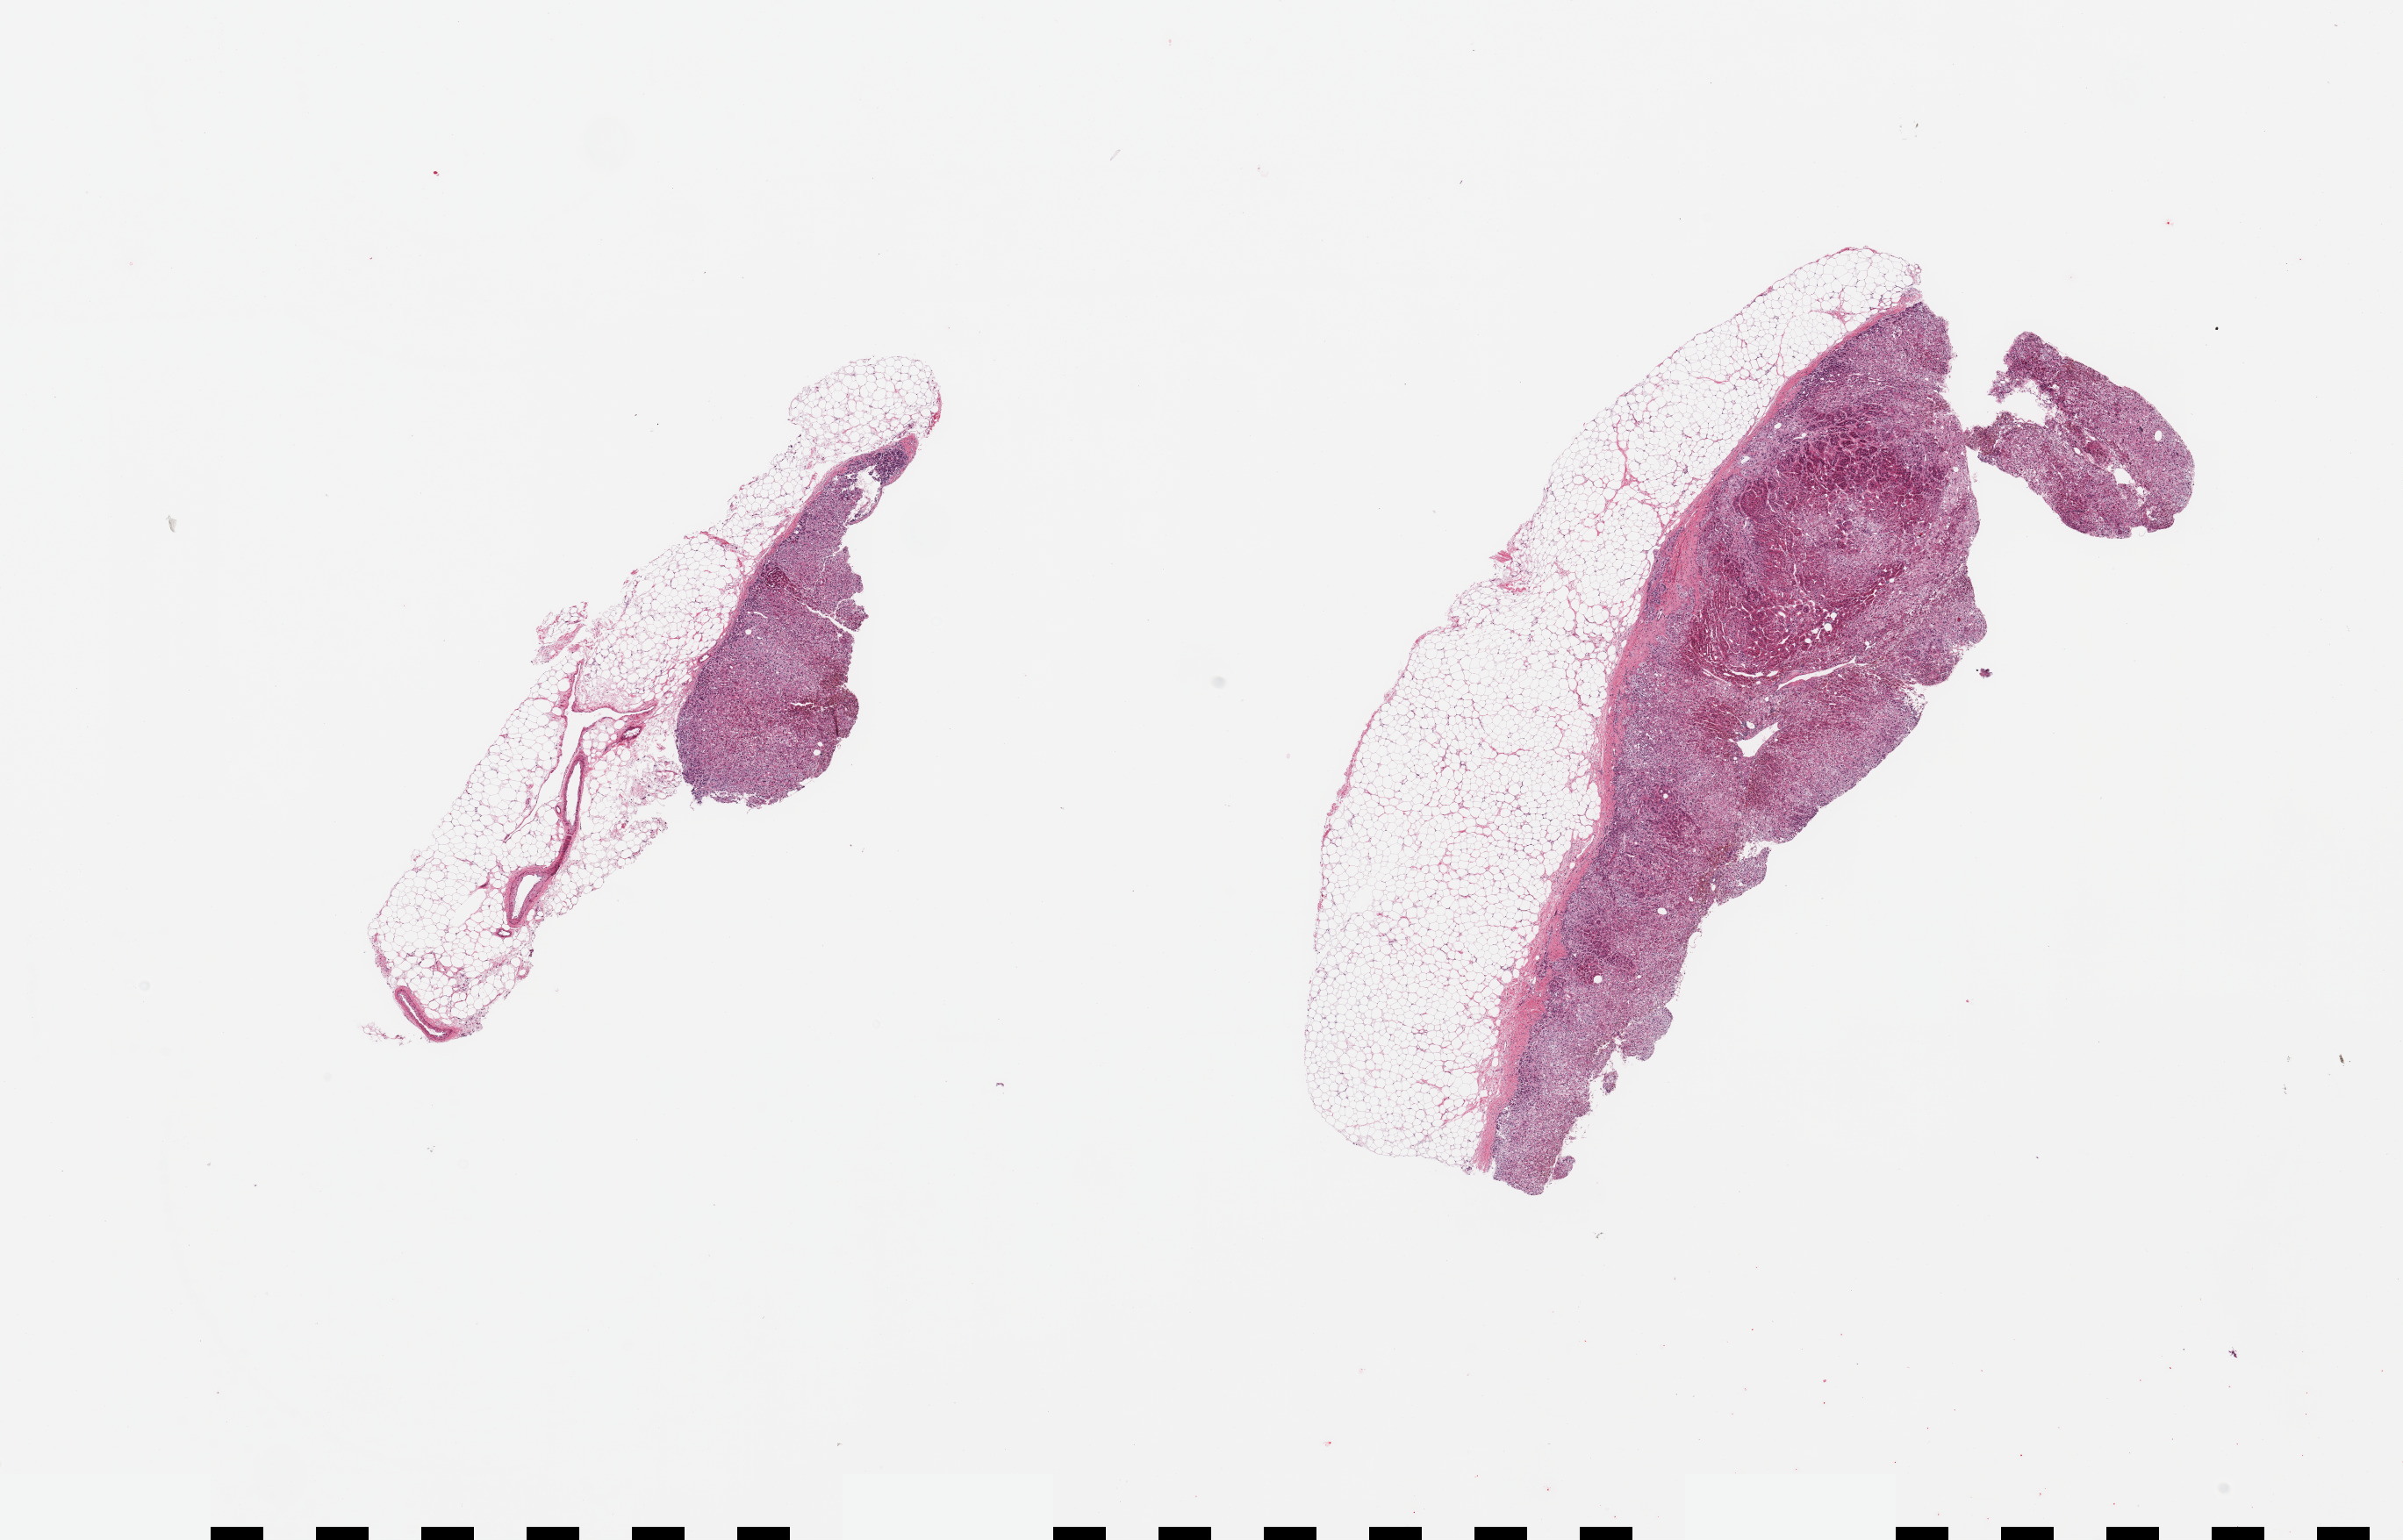
Digitized haematoxylin and eosin-stained section, brightfield, whole scanned area (about 21.7 x 13.9 mm, from a 20x scan) shown as a low-resolution overview. PAXgene-fixed, paraffin-embedded tissue. Sampled site (target tissue): adrenal gland. Tissue donor sample.
Pathologist's review note for this sample: 2 pieces, ~50% target, all cortex, moderately autolyzed; rest is adherent fat.